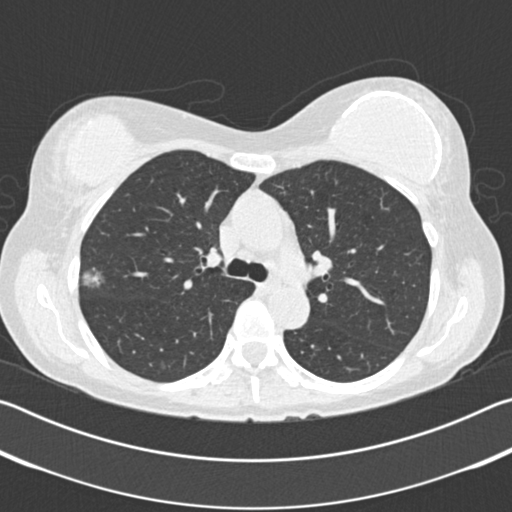
Low-dose screening chest CT, one axial slice. Slice 124 of 183 in the series (ordered by position). Reconstruction kernel B30f. Lung window (W 1500 / L -600 HU). 2 mm slice thickness. 512 × 512 image matrix, field of view 340 × 340 mm.
Structures marked on this image (outlined manually by an expert reader):
- lesion 1 (tumor, upper lobe of right lung): box from (x=81, y=270) to (x=105, y=288) px